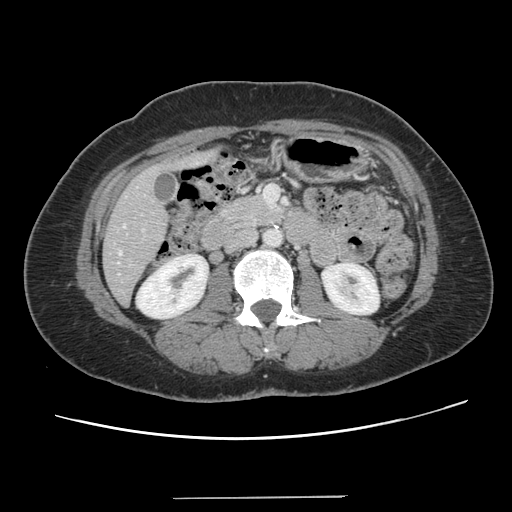
Contrast-enhanced abdominal CT, one axial slice; slice 44 of 141 in the series (ordered by position); 120 kVp; intravenous contrast given; soft-tissue window (W 400 / L 40 HU); 2.5 mm slice thickness; 512 × 512 image matrix, field of view 366 × 366 mm. Female patient, age 53 years. From the clinical record (not read from this slice): diagnosis: colorectal cancer liver metastases, imaged before liver resection; multiple liver metastases: no; largest metastasis: 14.5 cm; chemotherapy before resection: yes.
Outlined on this slice (expert manual segmentation):
- hepatic veins: box from (x=118, y=225) to (x=125, y=254) px
- liver: (x=104, y=153)–(x=212, y=303)
- planned liver remnant (the part of the liver to remain after resection): (x=104, y=217)–(x=167, y=304)